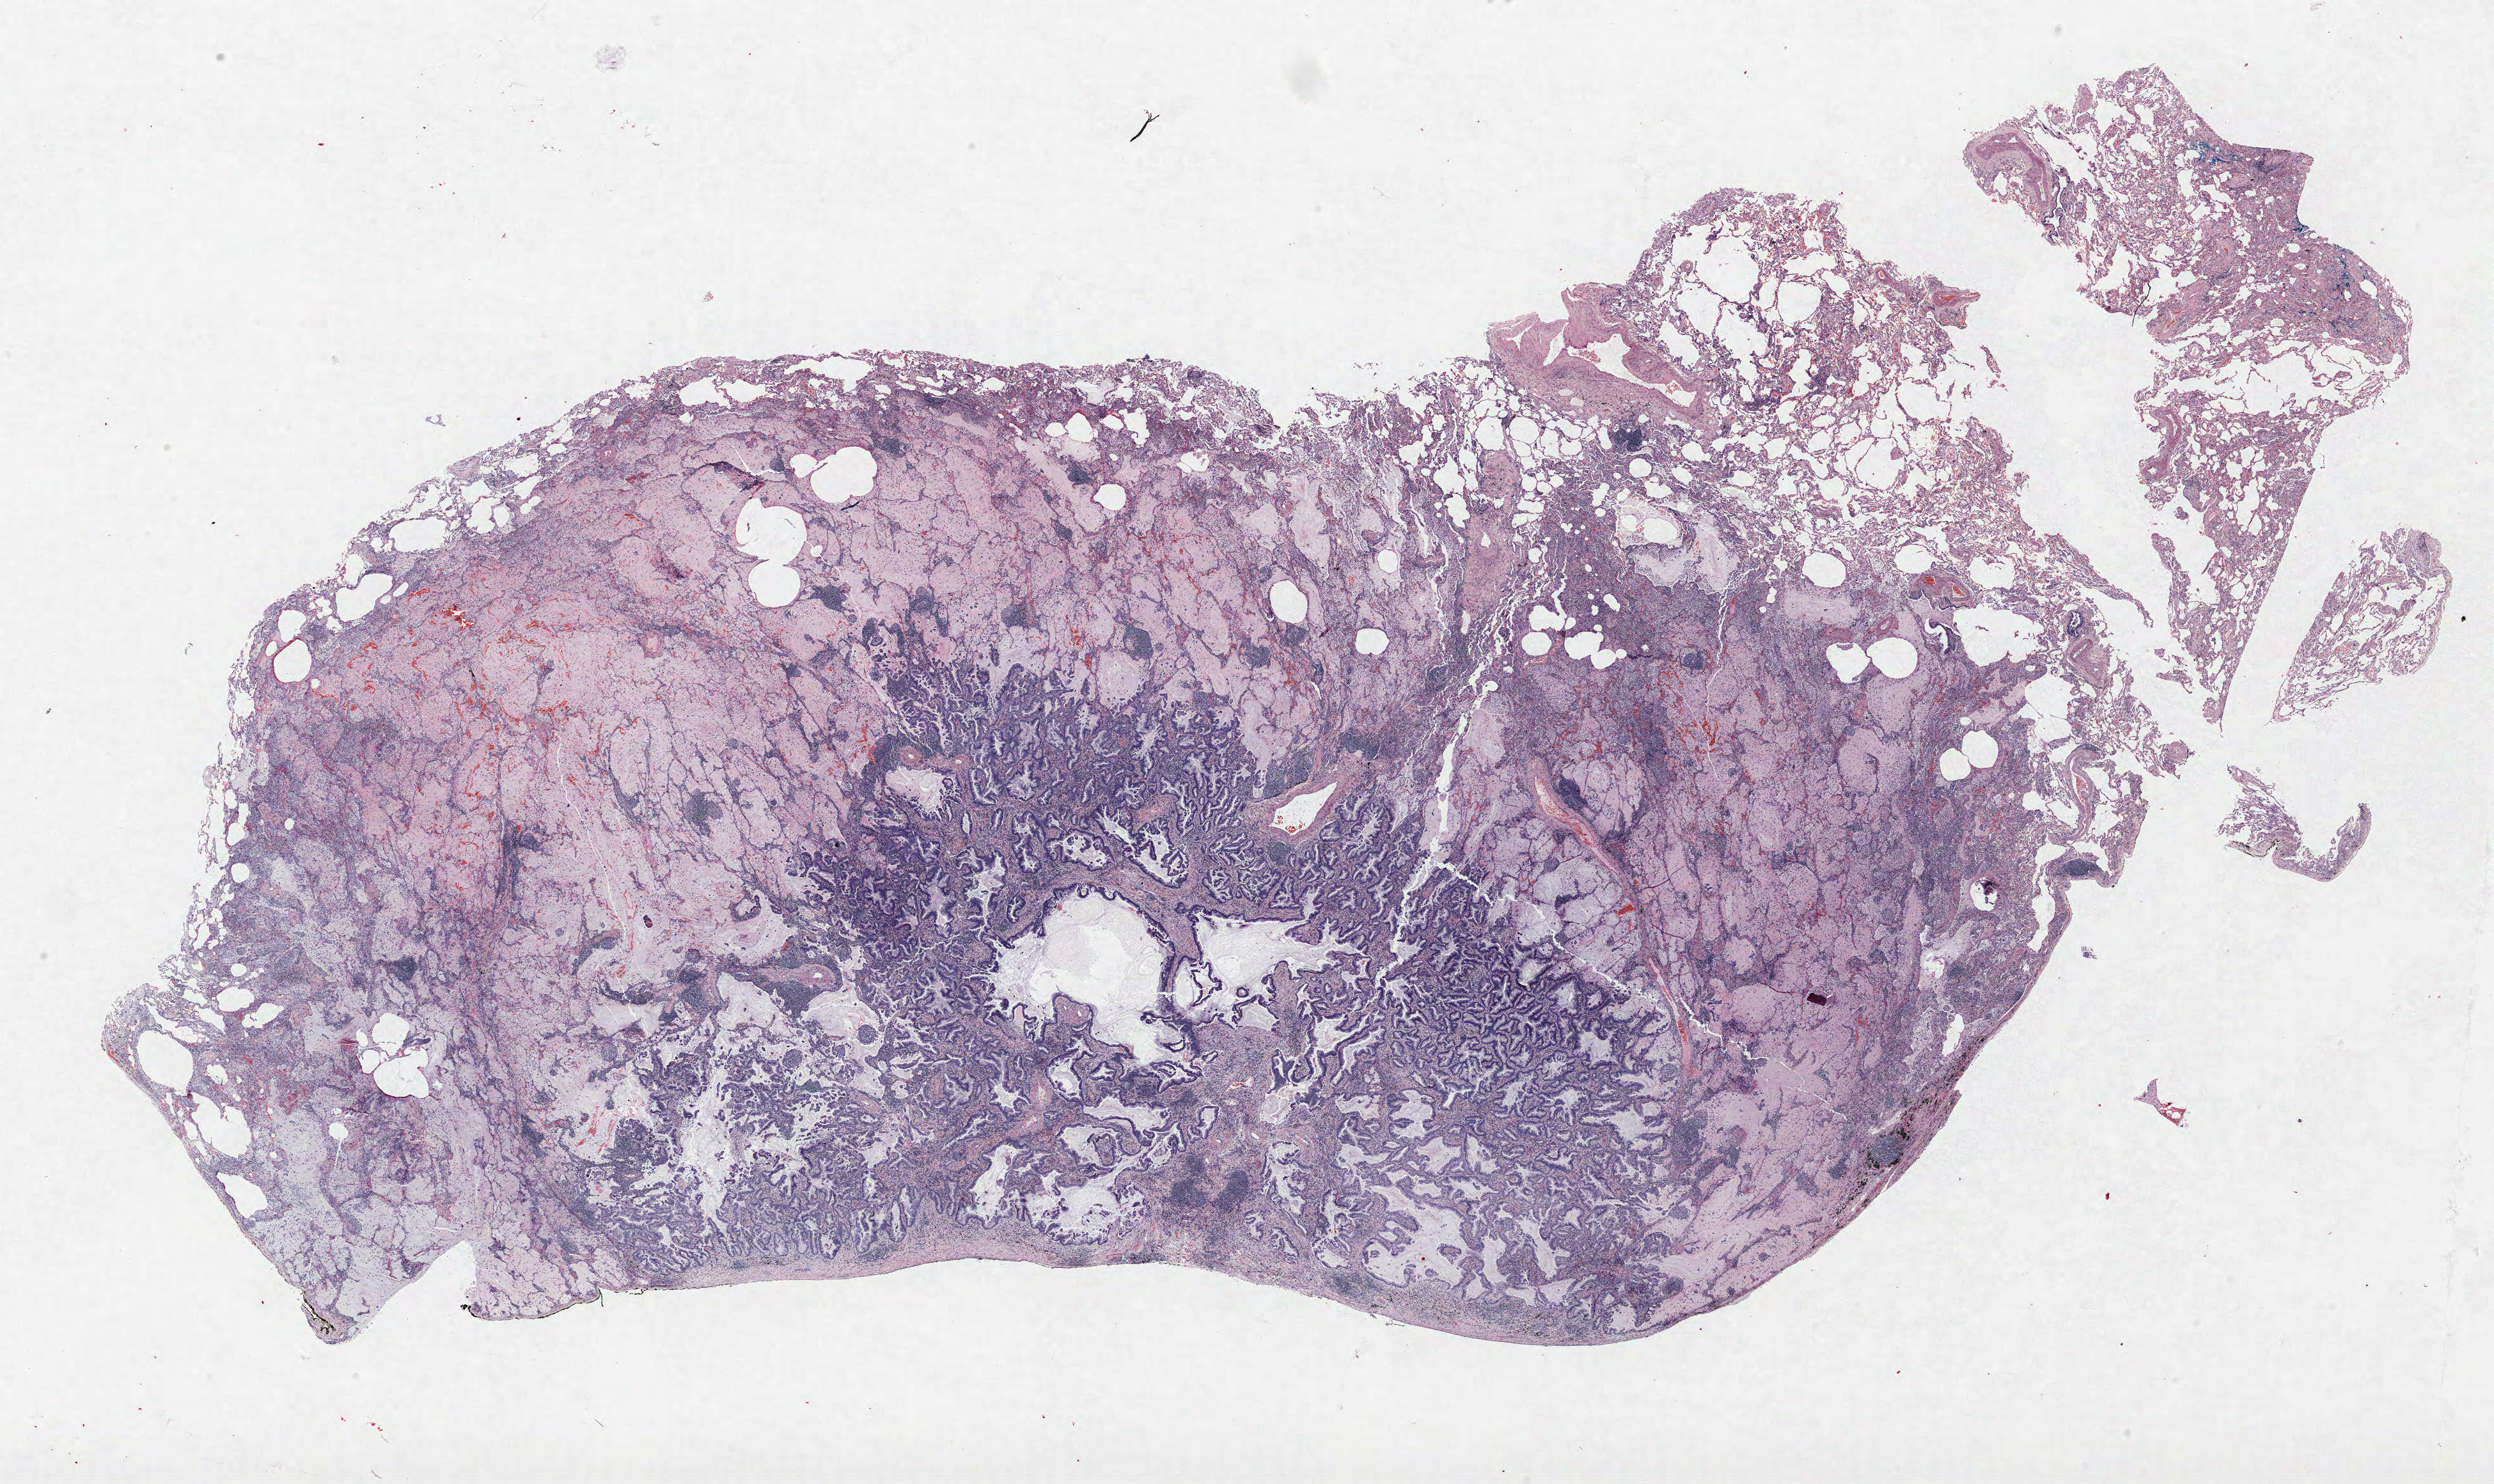
Whole-slide histology image, Hematoxylin and eosin (H&E) stained — whole scanned area (about 31.2 x 18.6 mm, slide scanned at 40x) shown as a low-resolution overview. FFPE section. Lung. Male, age 73 at enrolment. Grade: well differentiated (G1).
- tumour size (pathology): 18 mm
- primary tumour location (clinical record): right lower lobe
- ICD-O-3 topography: lower lobe of lung (C34.3)
- participant's lung-cancer diagnosis: Adenocarcinoma, NOS
- stage (AJCC 6th edition): IA